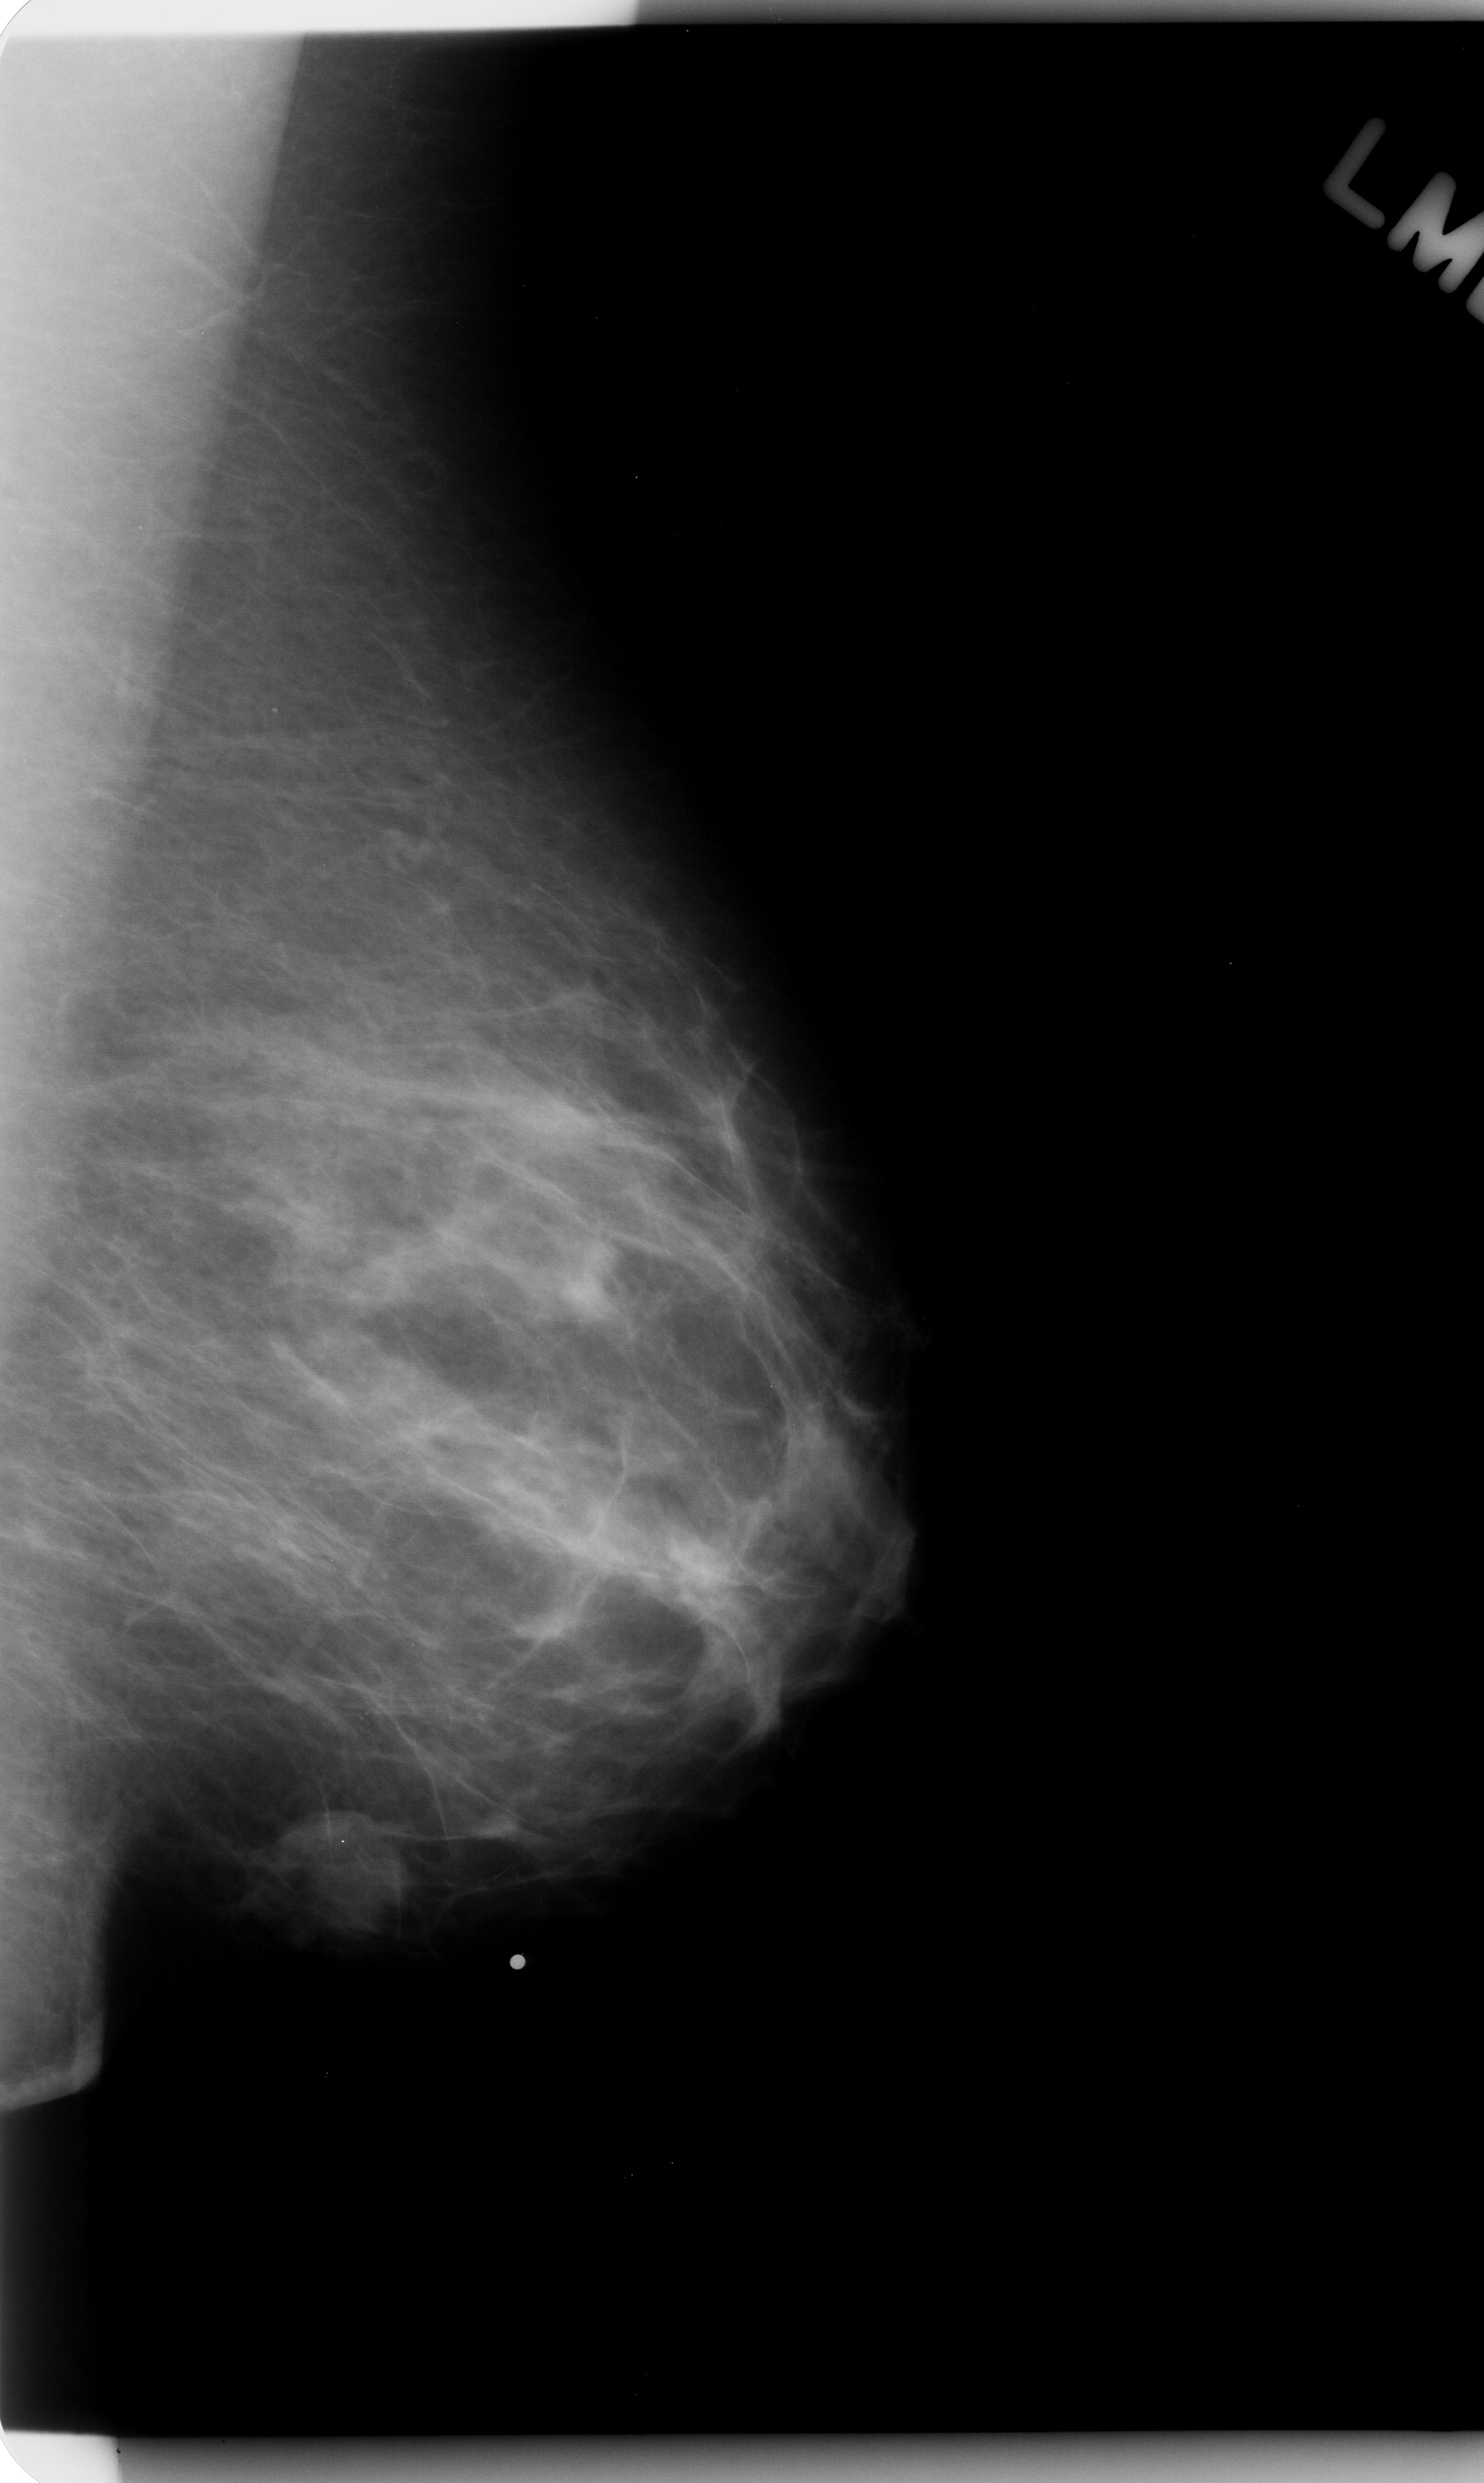
Mammogram (digitized film). Left breast. MLO view. Breast composition: scattered fibroglandular densities (BI-RADS density category 2 of 4). 1484 × 2483 image matrix.
Expert-marked regions of interest on this image (one box per marked abnormality):
- mass, shape lobulated, margins microlobulated; BI-RADS assessment category 5; pathology result (as recorded, not read from the image): malignant: box from (x=193, y=1746) to (x=458, y=1965) px